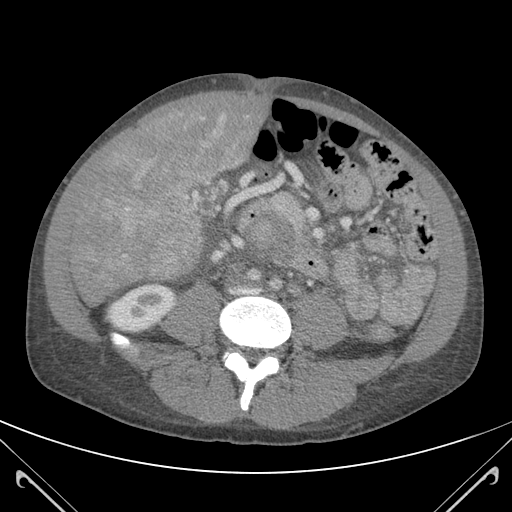
Contrast-enhanced abdominal CT (liver protocol), one axial slice; position 34 of 118 along the scan axis; 120 kVp; soft-tissue window (W 400 / L 40 HU); 3 mm slice thickness; 512 × 512 image matrix, field of view 380 × 380 mm. From the clinical record (not read from this slice): diagnosis: hepatocellular carcinoma (patient treated with transarterial chemoembolisation; whether this scan precedes or follows treatment is not stated here); TNM stage (as recorded): Stage-IIIB.
Outlined on this slice (semi-automatically segmented with operator editing):
- mass: bounding box [x1, y1, x2, y2] px = [87, 93, 255, 278]